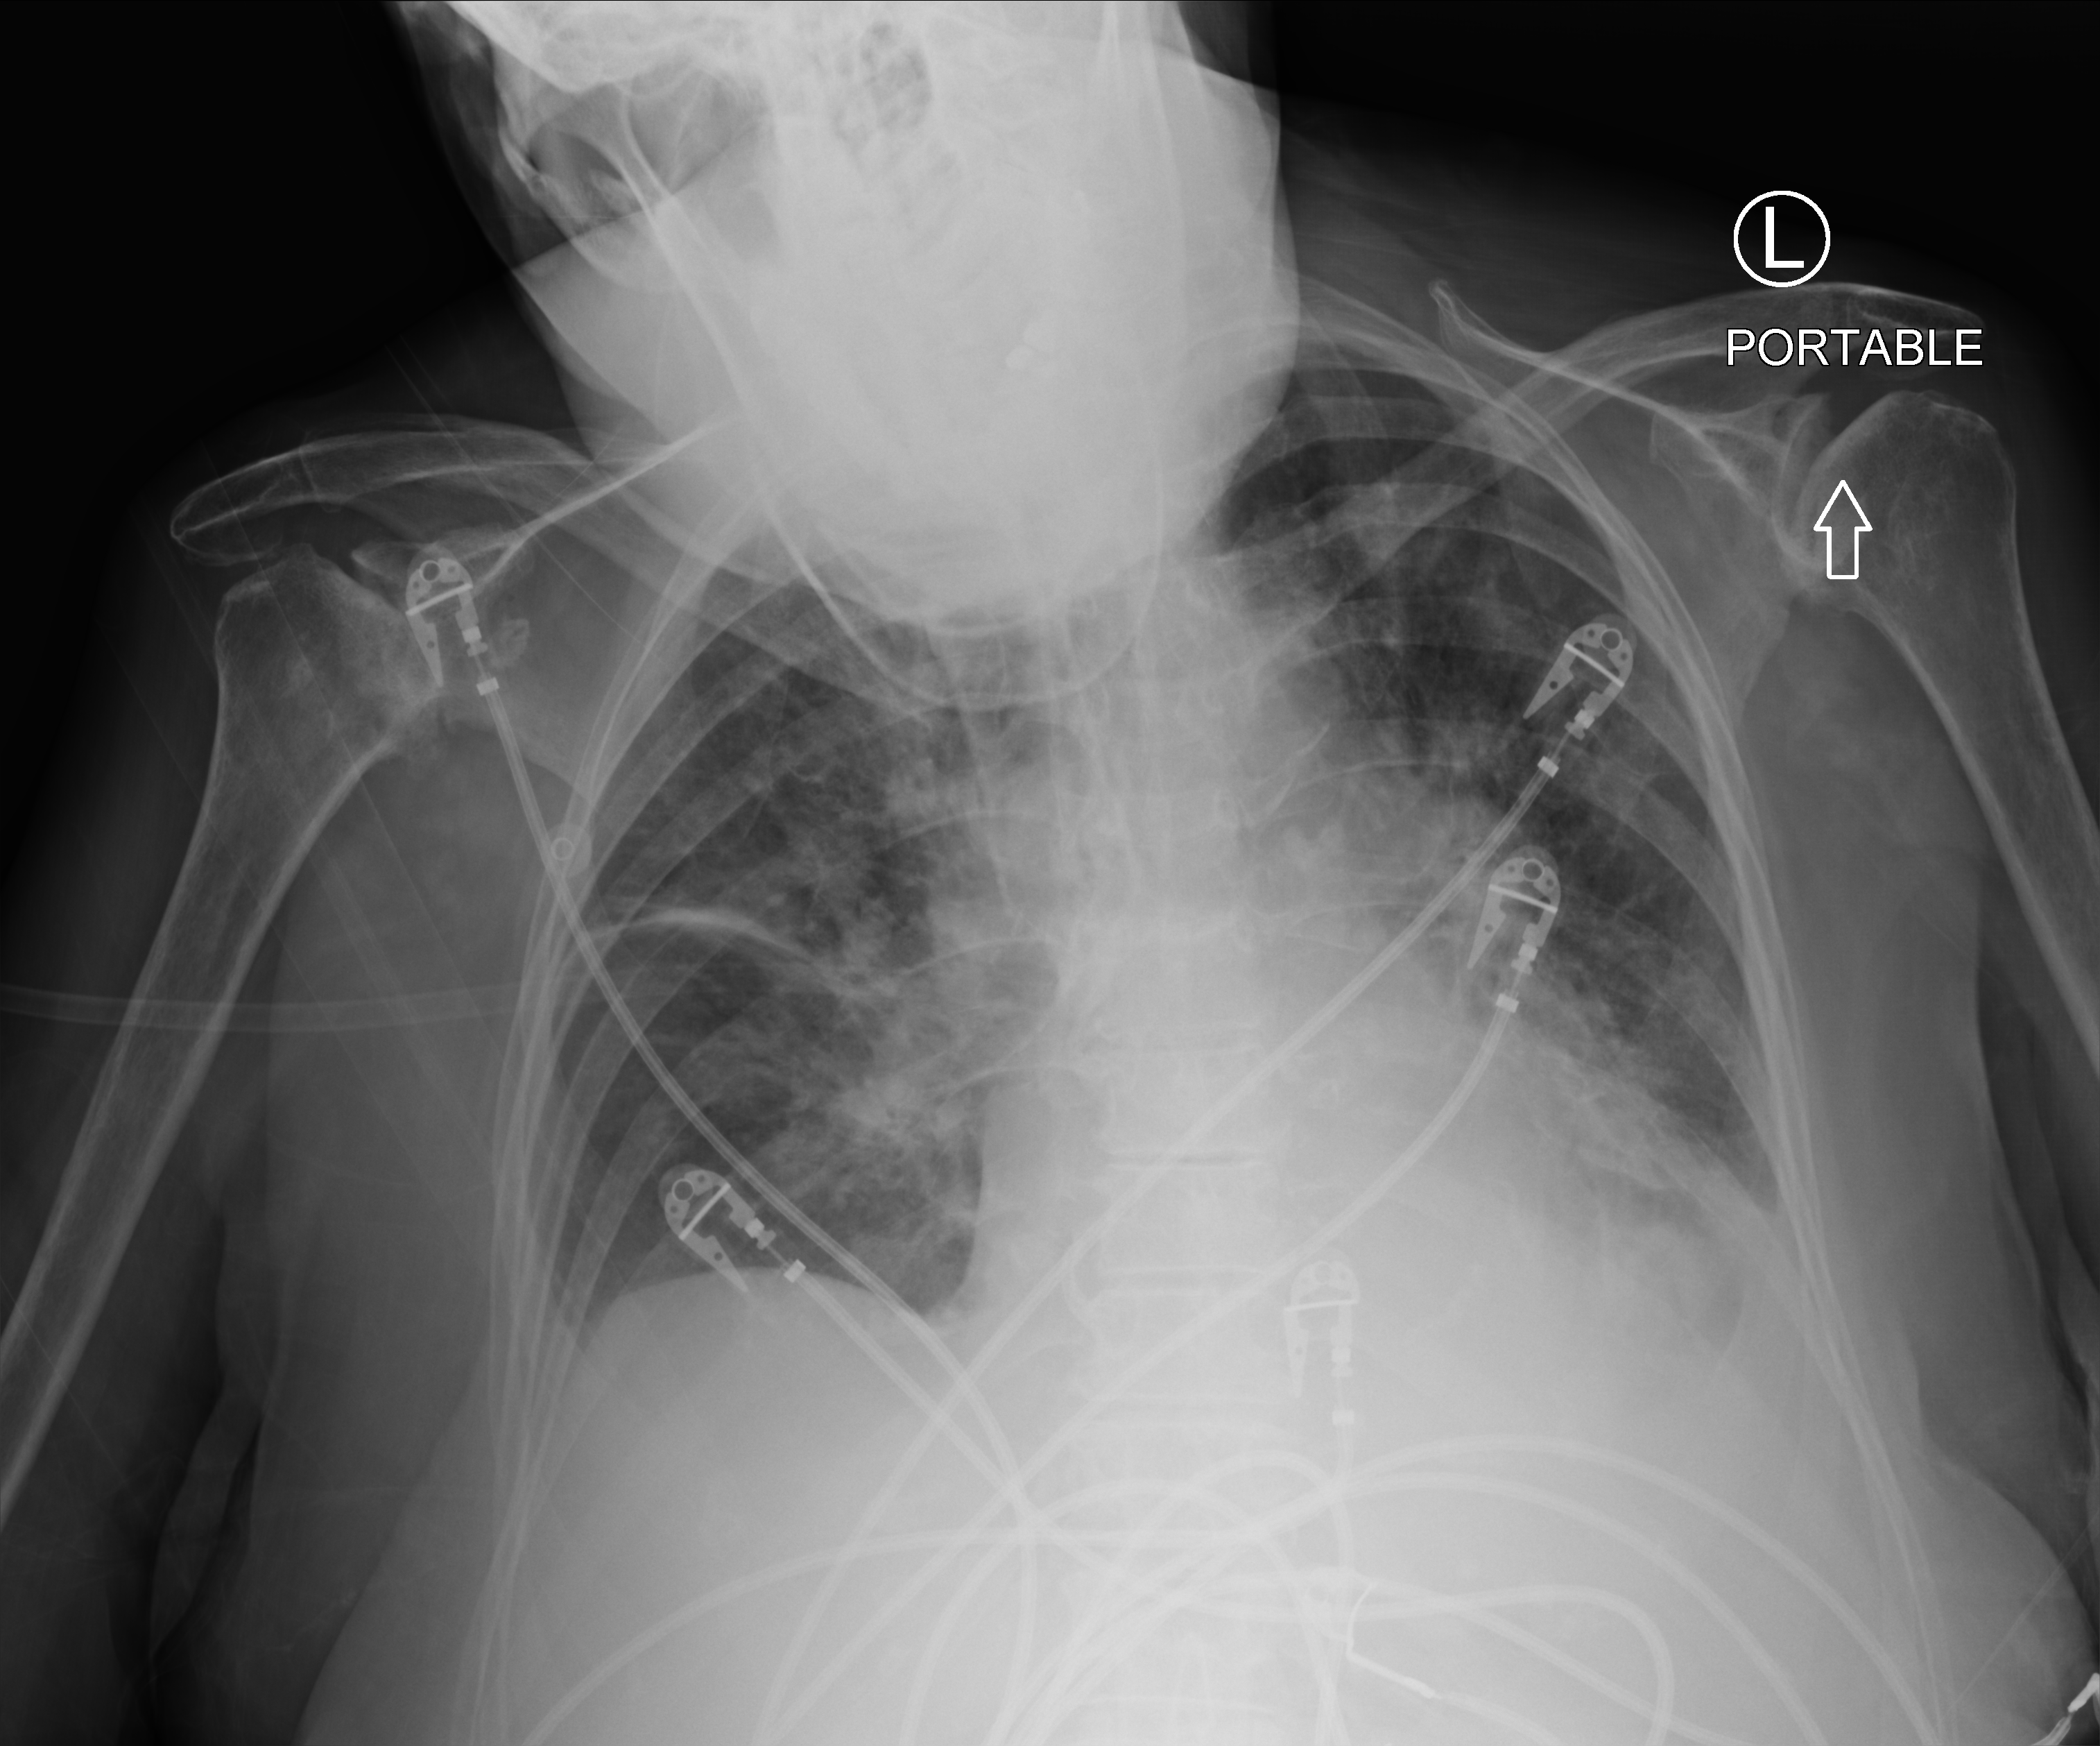
Bedside chest radiograph (computed radiography); anteroposterior (AP) projection. Patient hospitalised with COVID-19; female, aged 75–90 years.
Admission-level facts for this patient (not findings on this image; timing relative to this image not recorded):
- mechanically ventilated during this hospital stay: no
- admitted to intensive care during this hospital stay: no